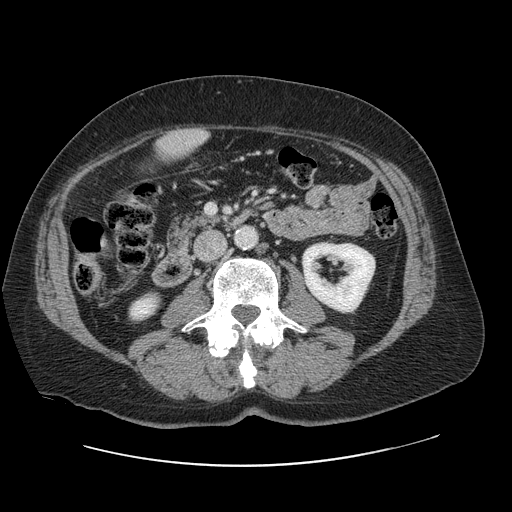
Contrast-enhanced abdominal CT, one axial slice. Position 15 of 138 along the scan axis. Intravenous contrast given. Soft-tissue window (W 400 / L 40 HU). 2.5 mm slice thickness. 512 × 512 image matrix, field of view 402 × 402 mm. Male patient, age 71 years. From the clinical record (not read from this slice): diagnosis: colorectal cancer liver metastases, imaged before liver resection; multiple liver metastases: no; largest metastasis: 3.3 cm; disease in both lobes: no.
Annotated regions visible in this slice (expert manual segmentation):
- liver: bounding box <156,130,207,162> (left, top, right, bottom; pixels)